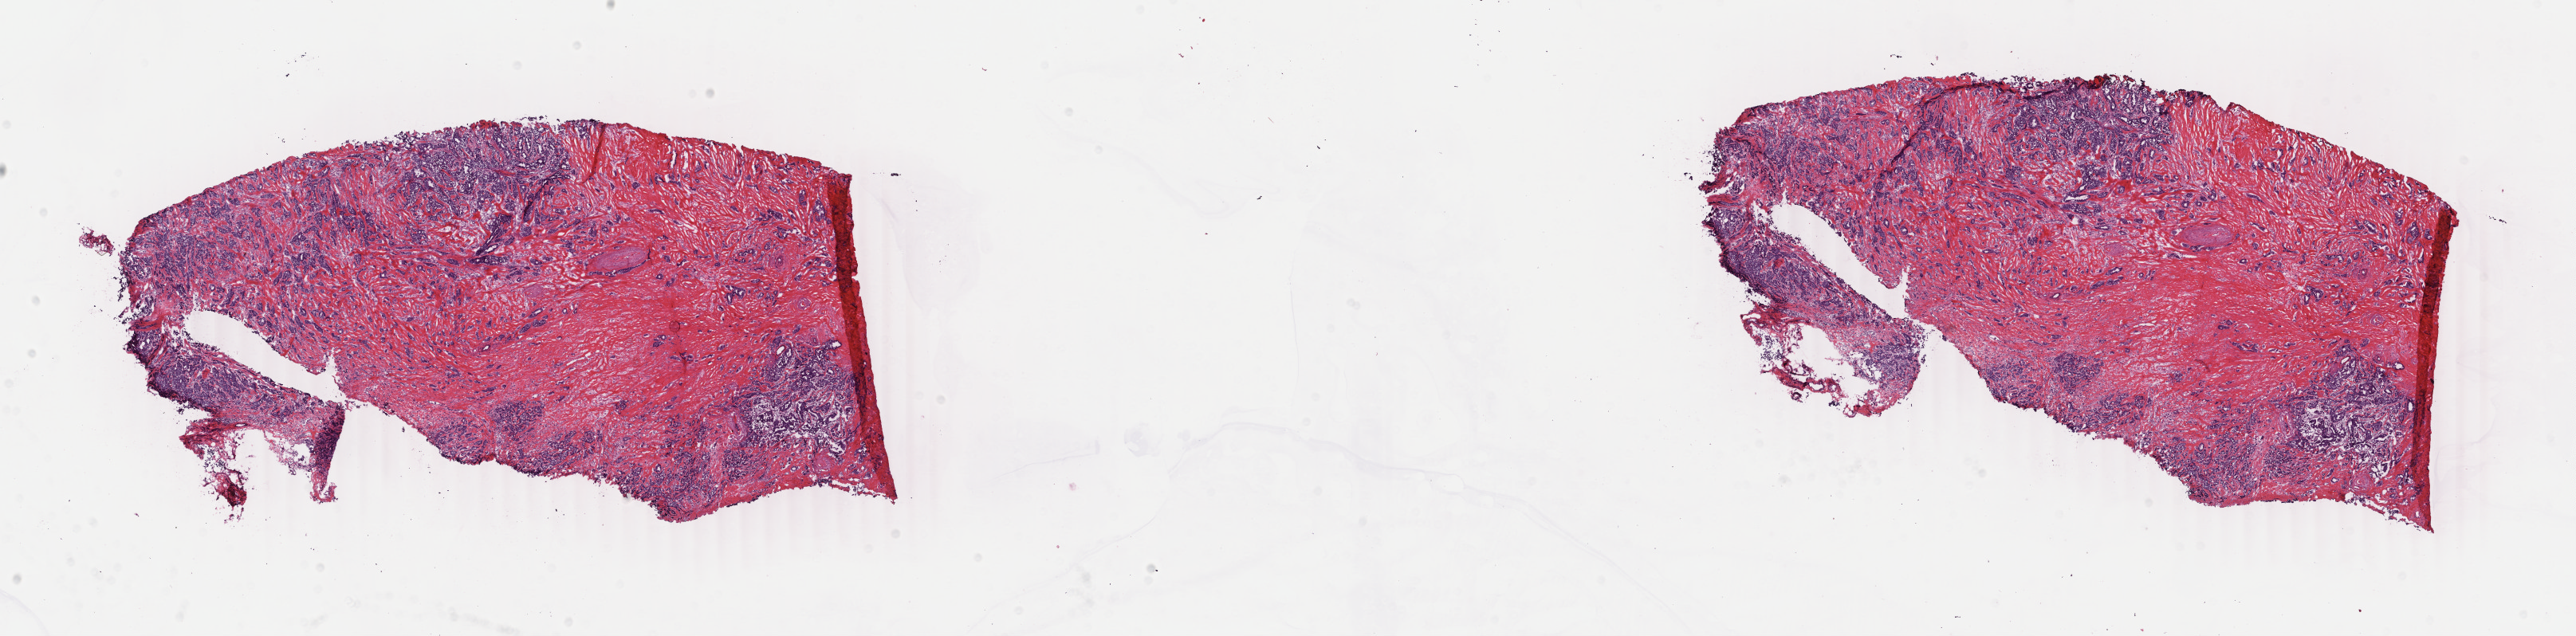
Digitized H&E tissue section (whole slide) — whole scanned area (about 25.7 x 6.3 mm, slide scanned at 40x) shown as a low-resolution overview, frozen section from the bottom of the tissue portion, primary tumour sample from the breast. Patient: female, age at initial diagnosis 73 years. Pathologist review of this section (percent, as recorded): tumour cells 70%, tumour nuclei 85%.
Histologic diagnosis: Infiltrating duct and lobular carcinoma.